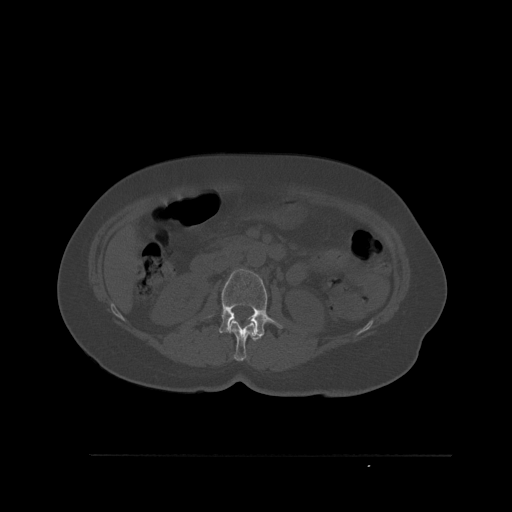
CT including the spine, one axial slice; slice 252 of 527 in the series (ordered by position); bone window (W 1800 / L 400 HU); 1.5 mm slice thickness; 512 × 512 image matrix, field of view 470 × 470 mm. Female patient, age 73 years. From the clinical record (not read from this slice): primary cancer: breast.
Annotated regions visible in this slice (semi-automatically segmented with operator editing):
- L1 vertebra: bounding box <228,319,257,361> (left, top, right, bottom; pixels)
- L2 vertebra: <209,268,283,340>